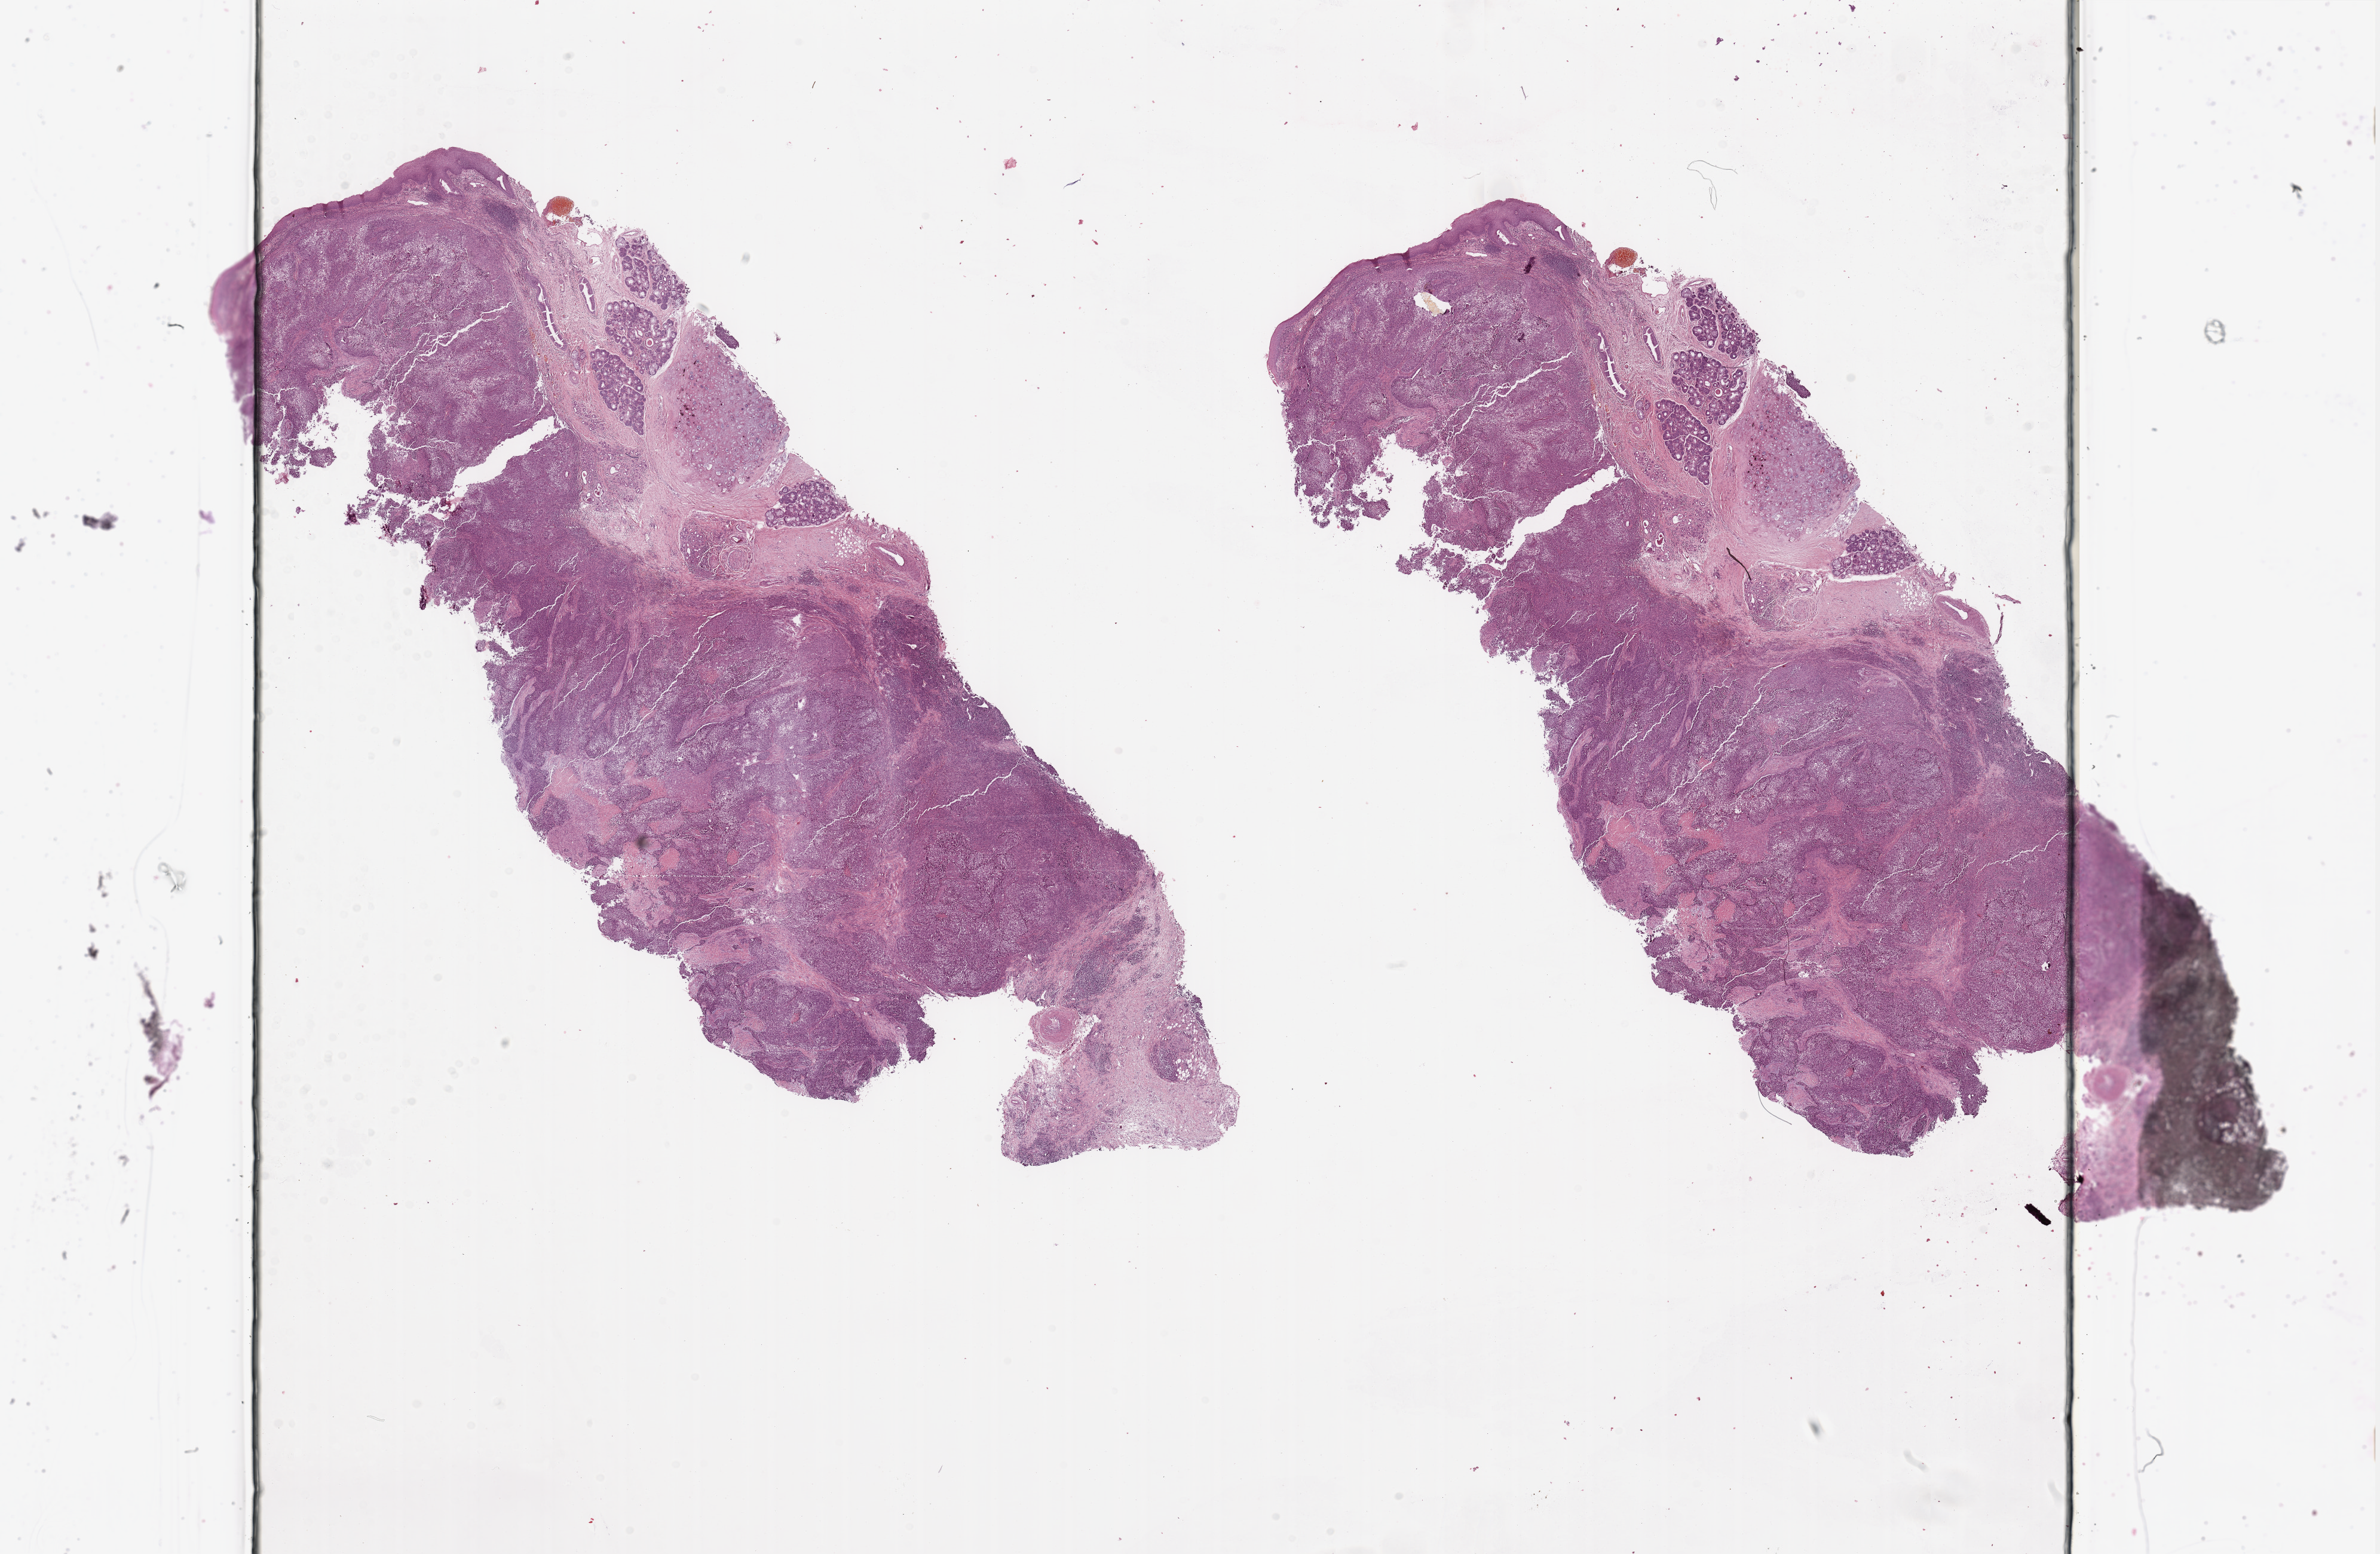
Whole-slide histology image, H&E — whole scanned area (about 31.5 x 20.6 mm) shown as a low-resolution overview. Head and neck, tissue type not recorded. Male, 64 y/o.
• patient diagnosis: Squamous cell carcinoma, NOS (larynx, NOS)